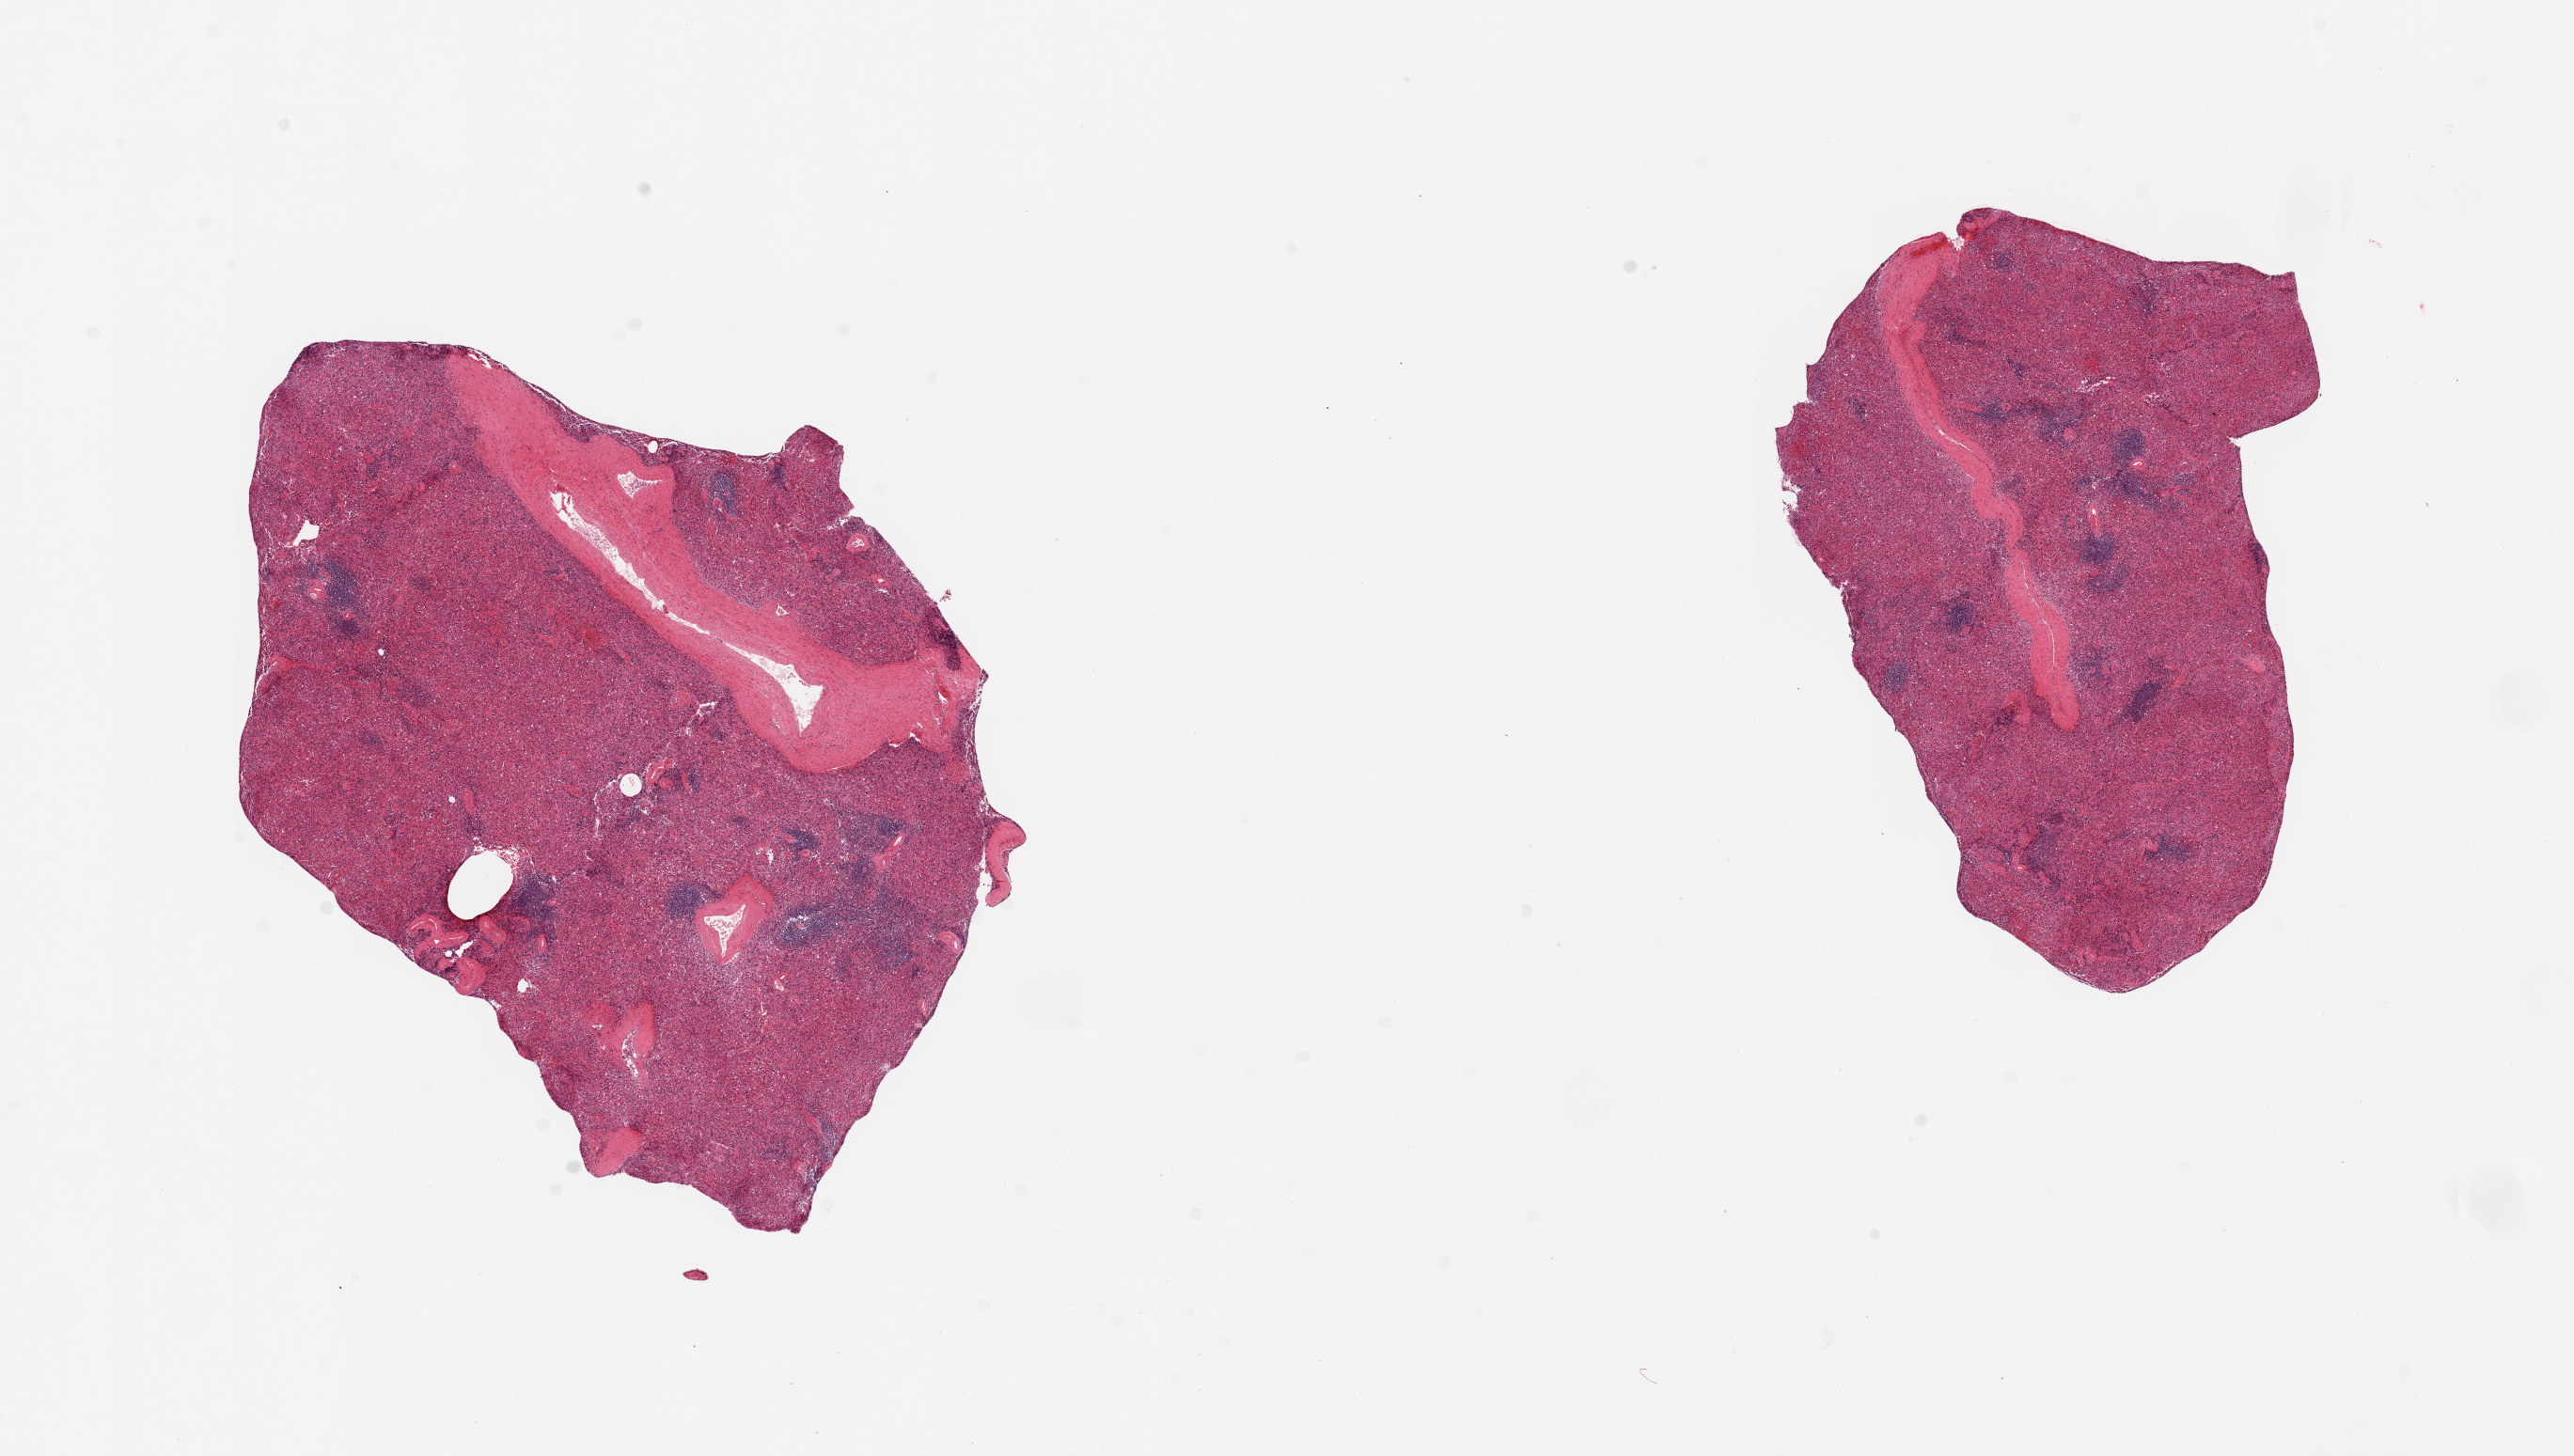
Haematoxylin and eosin whole-slide image, whole scanned area (about 21.7 x 12.3 mm) shown as a low-resolution overview, PAXgene-fixed paraffin-embedded (PFPE) section, sampled site (target tissue): spleen, tissue donor sample. Donor: female.
Review note (as recorded): 2 pieces; large artery occupies 10-20%.